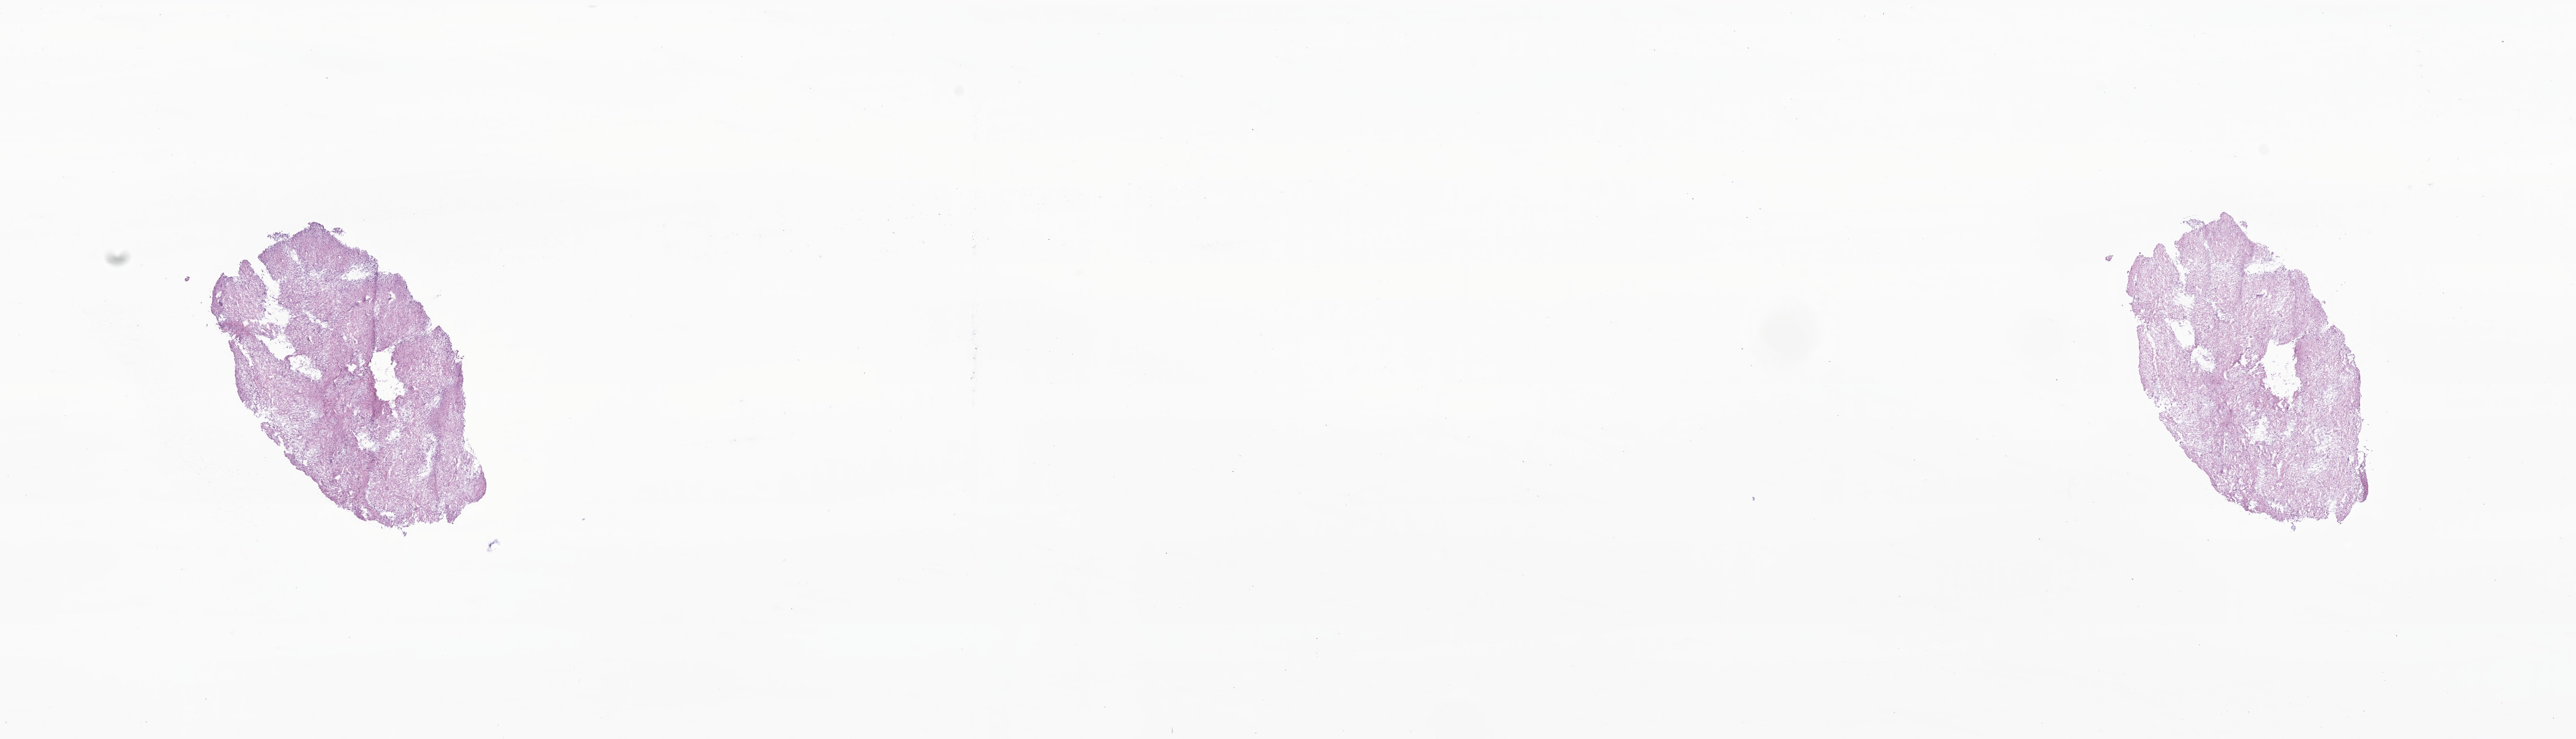
Digitized haematoxylin and eosin-stained section of tumor tissue from the brain, low-resolution overview of the scanned area, about 22.9 x 6.6 mm; cryosection (OCT / tissue freezing medium). Patient male; age 52 months (4 years 4 months).
Diagnosis: Pilocytic astrocytoma.